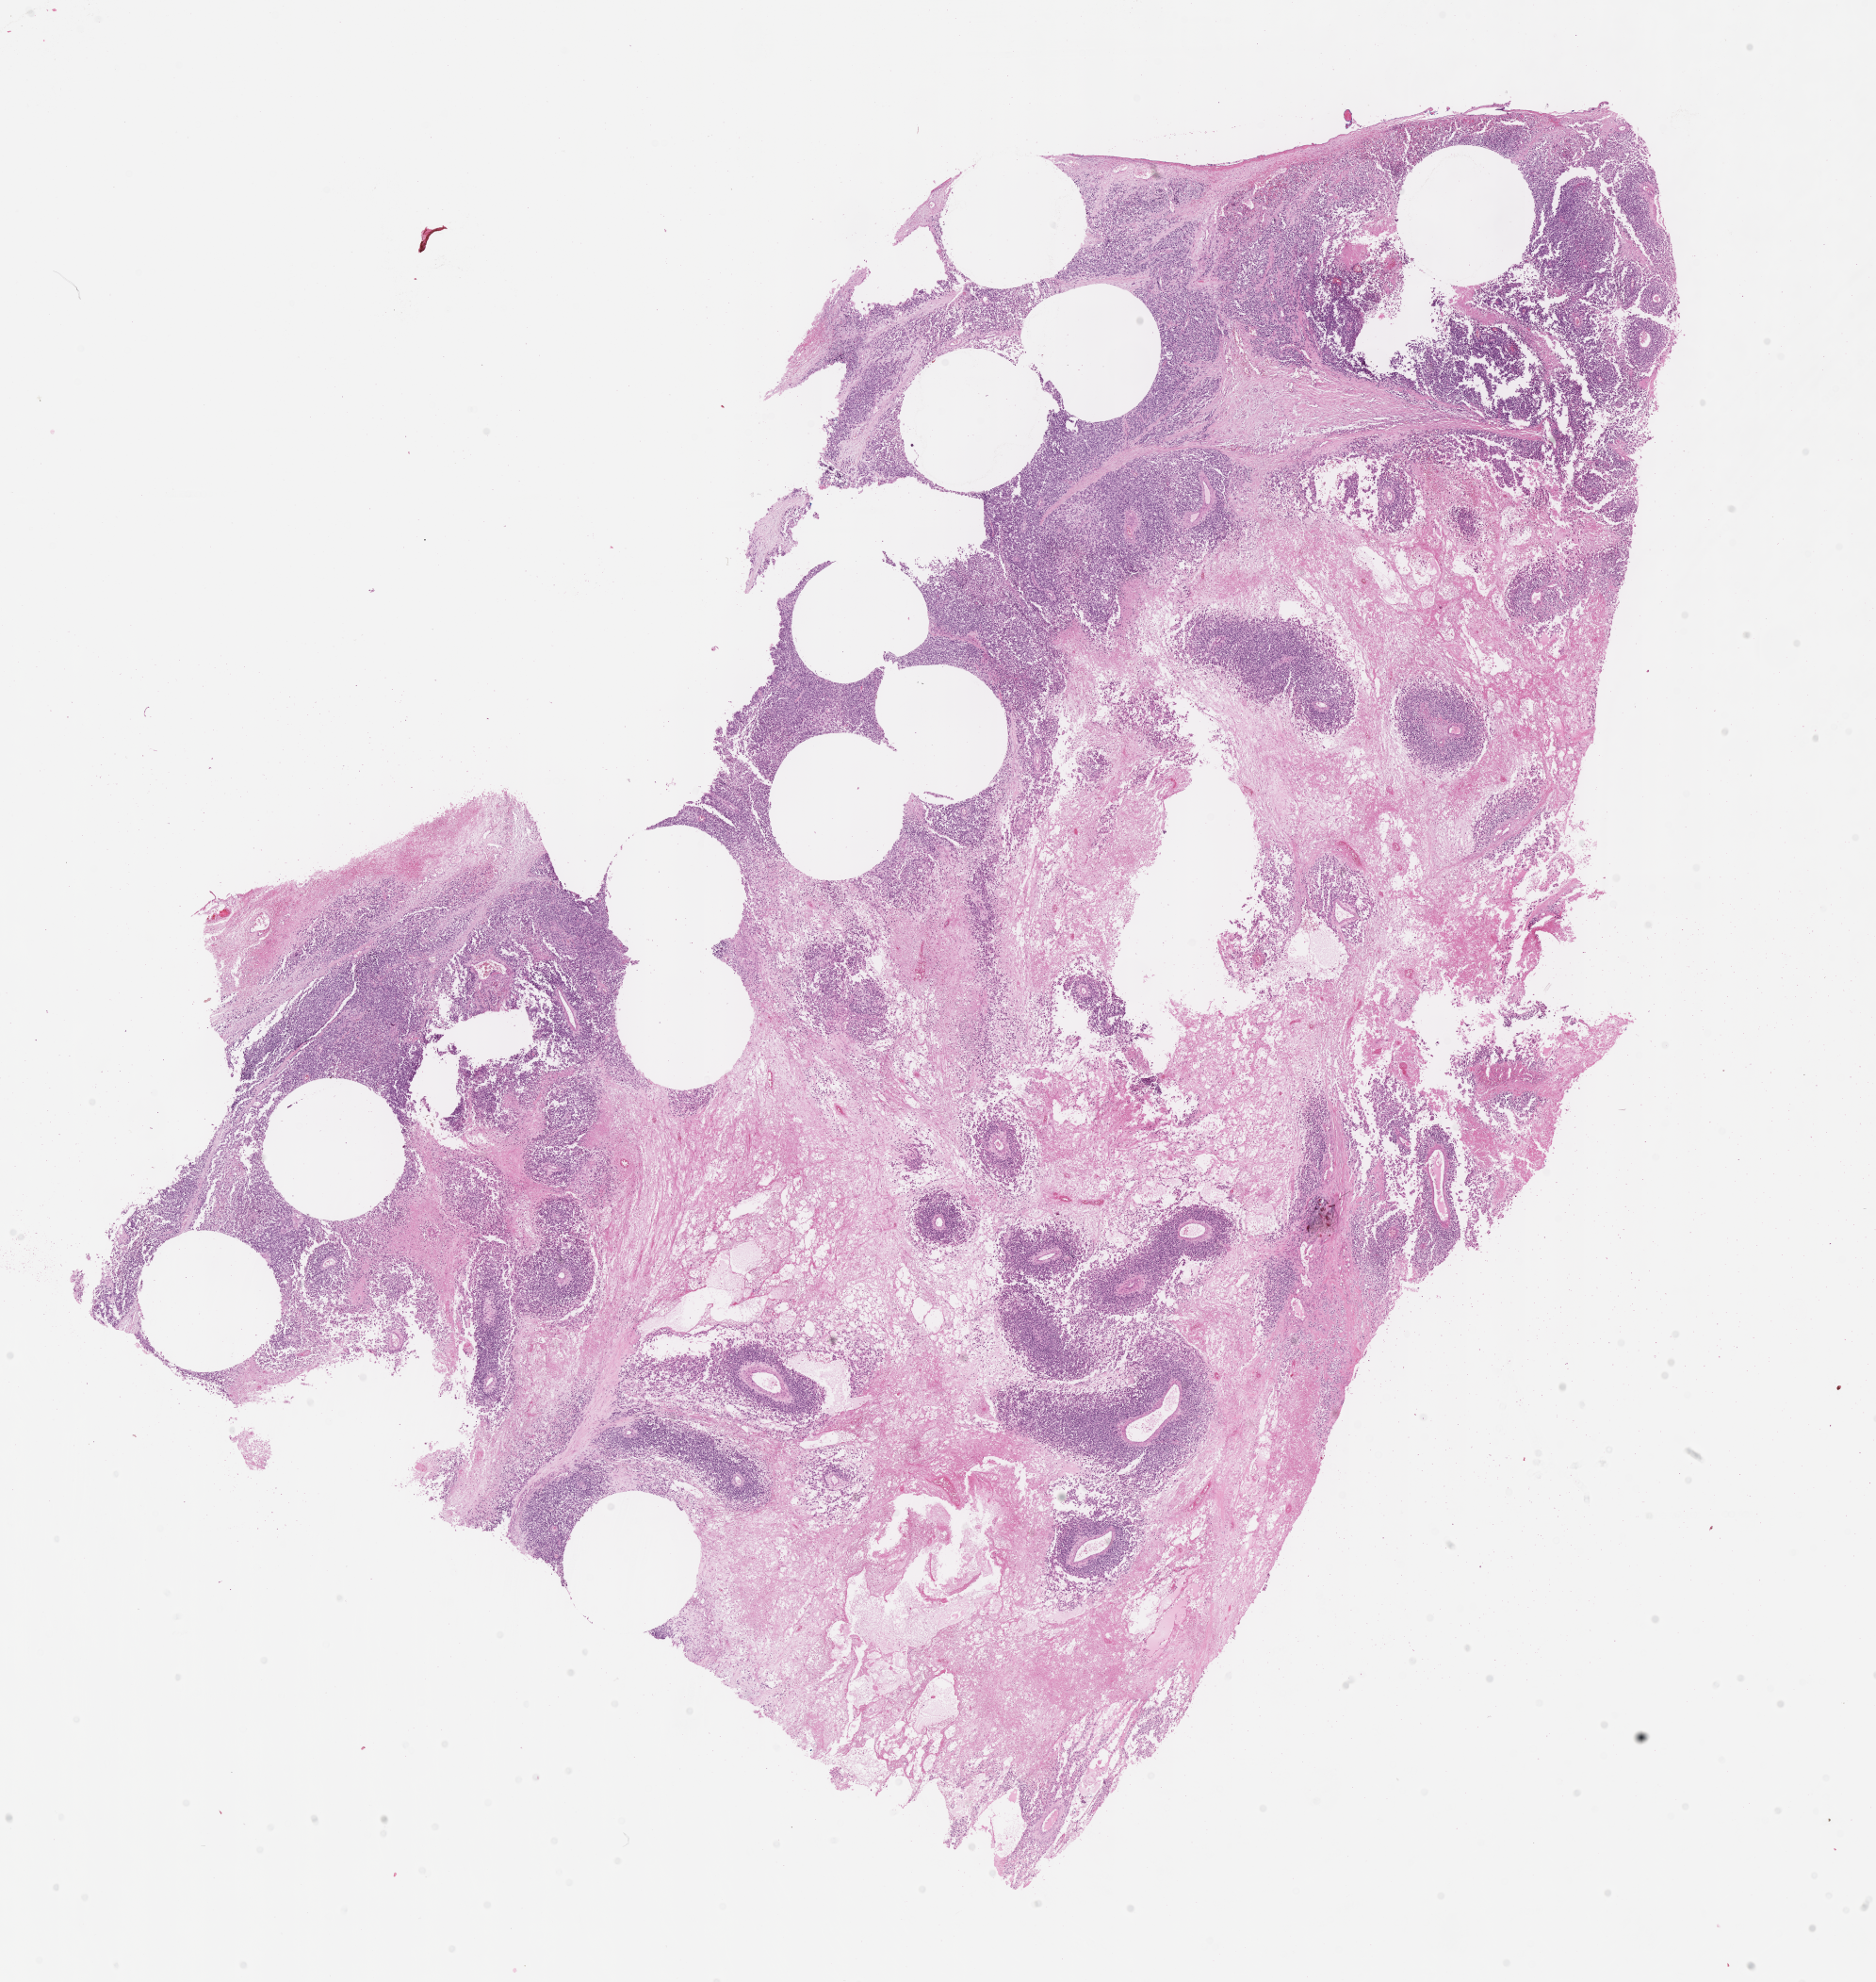
H&E whole-slide image of tumor tissue, whole scanned area (about 16.1 x 17.0 mm) shown as a low-resolution overview, FFPE section, sample anatomic site: mediastinum. Patient: male, age 18.4 years at diagnosis.
Diagnosis: rhabdomyosarcoma; histological classification: alveolar rhabdomyosarcoma.